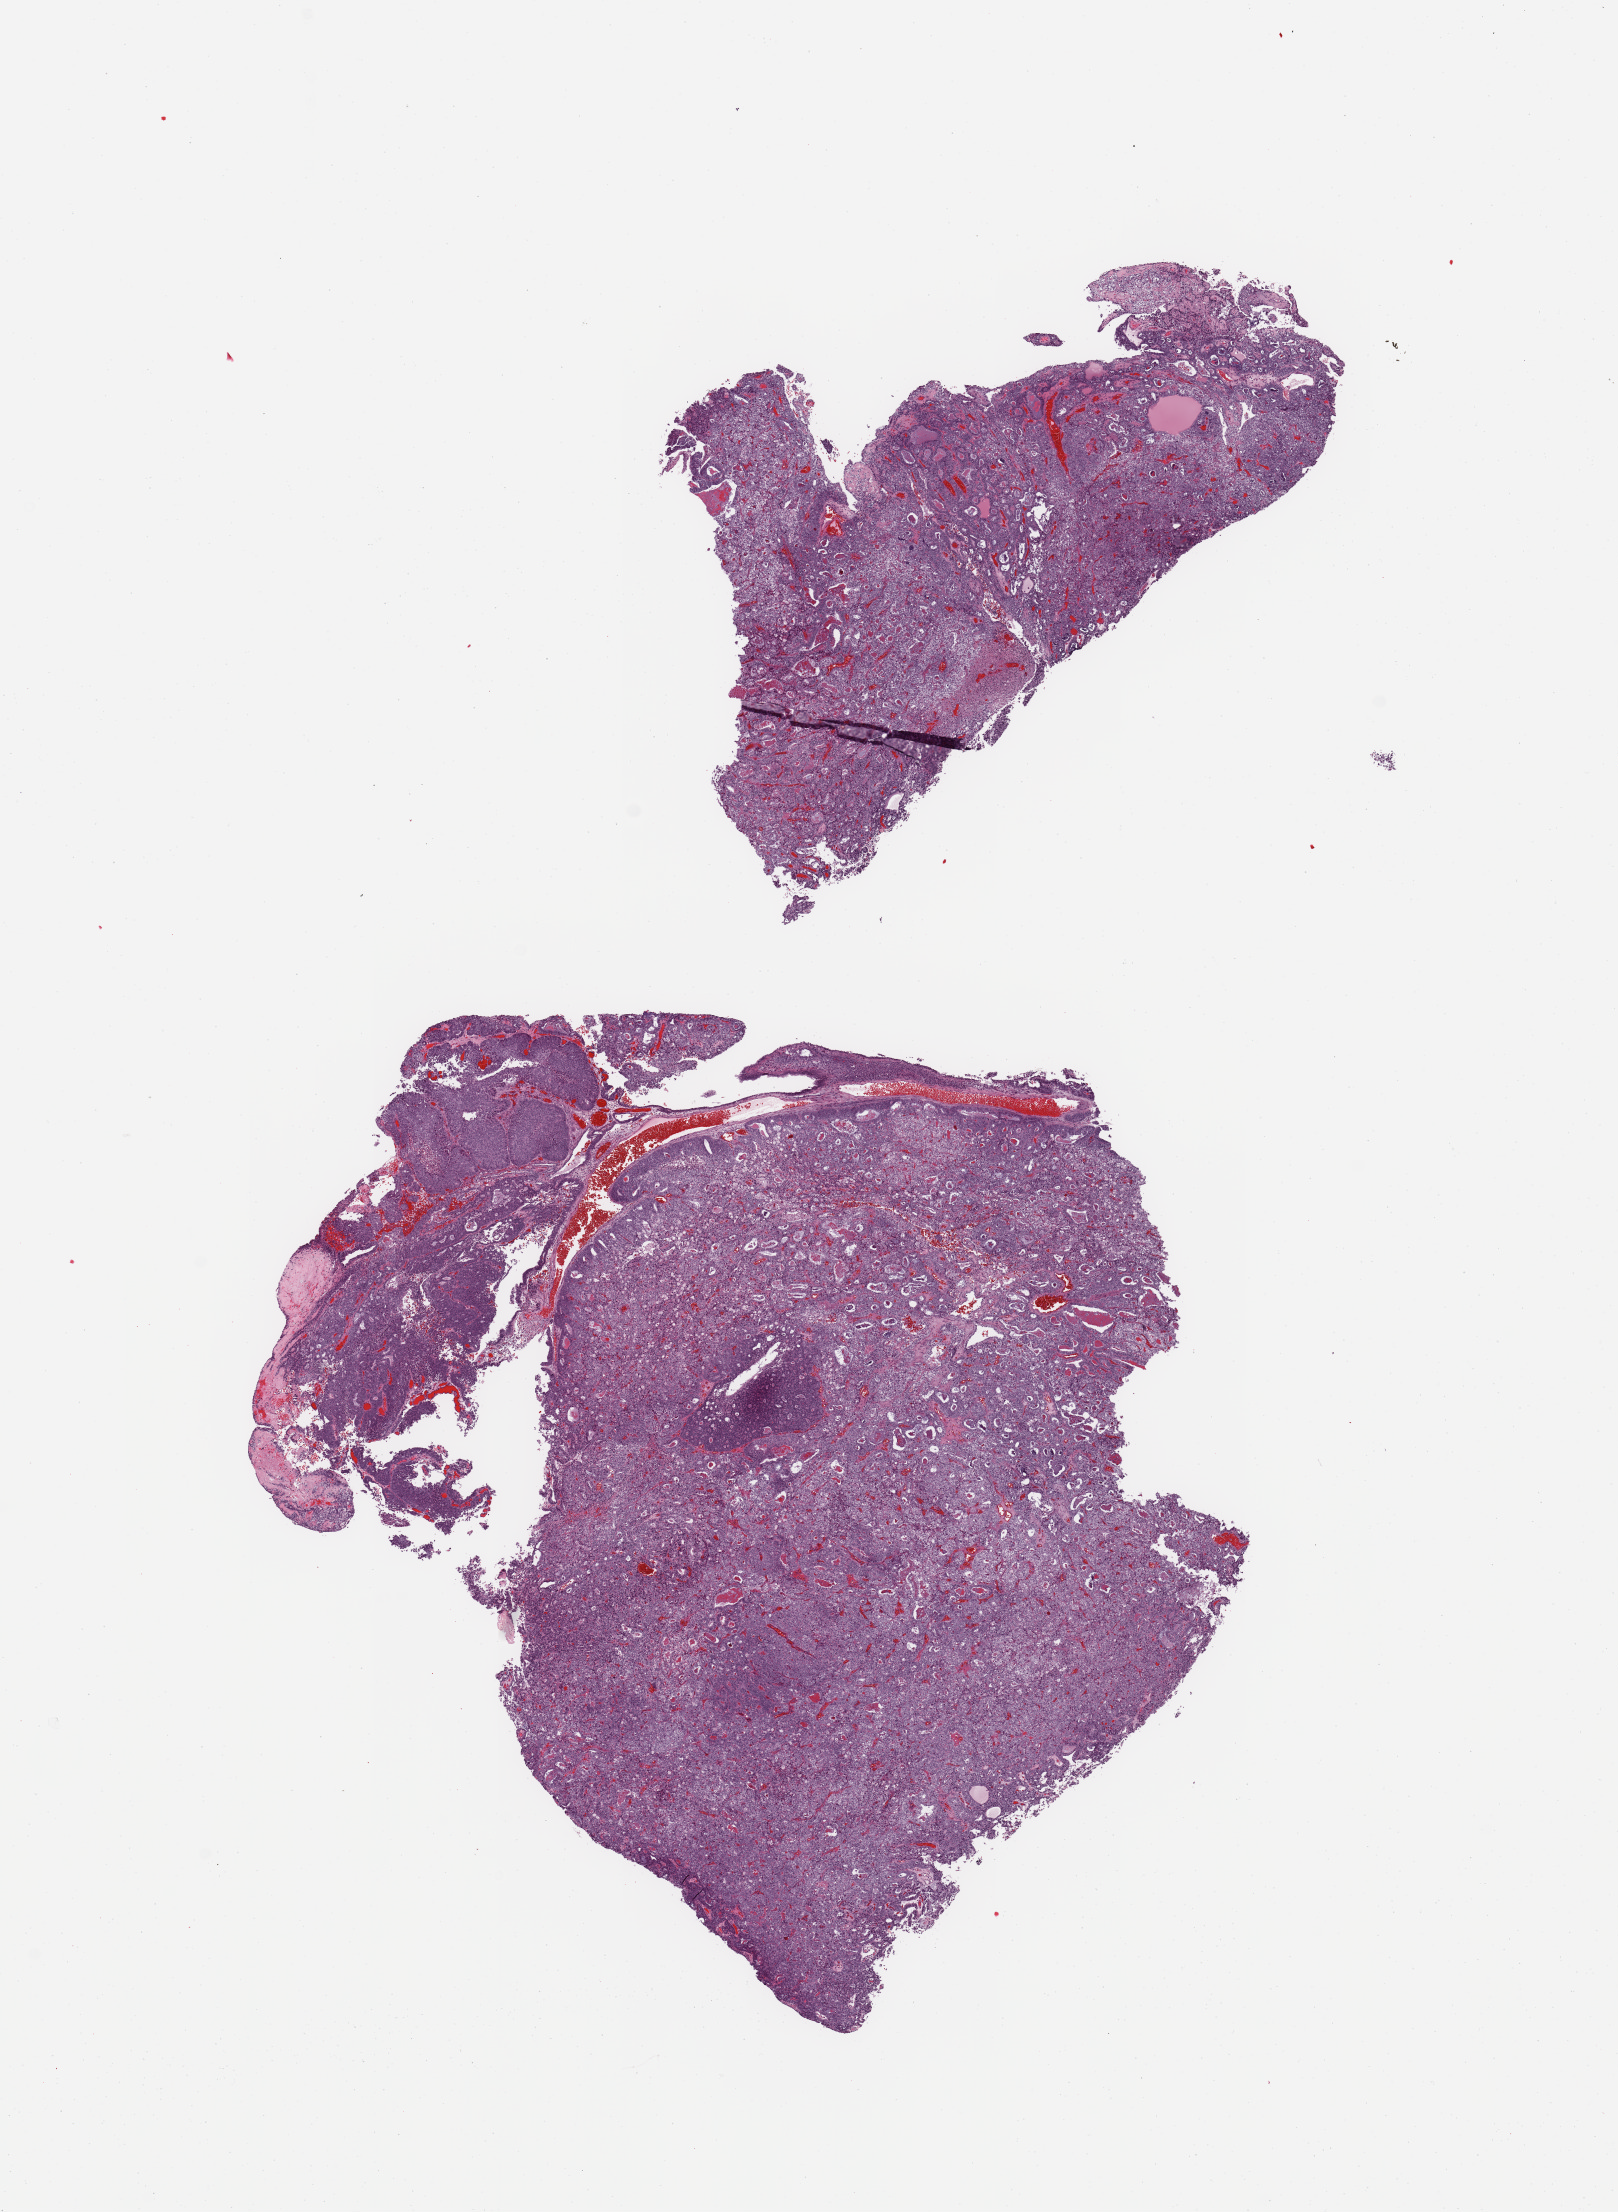
Digitized H&E-stained tissue section (whole slide), whole scanned area (about 12.8 x 17.5 mm, acquisition: 20x scan) shown as a low-resolution overview, tumour tissue sample, sampled site: uterus. 57-year-old female patient. Histologic grade: G3 (poorly differentiated). Pathologist review of this section (percent, as recorded): tumour nuclei 98%, necrosis 2%.
- AJCC pathologic stage: I
- histologic diagnosis: Endometrioid adenocarcinoma, NOS